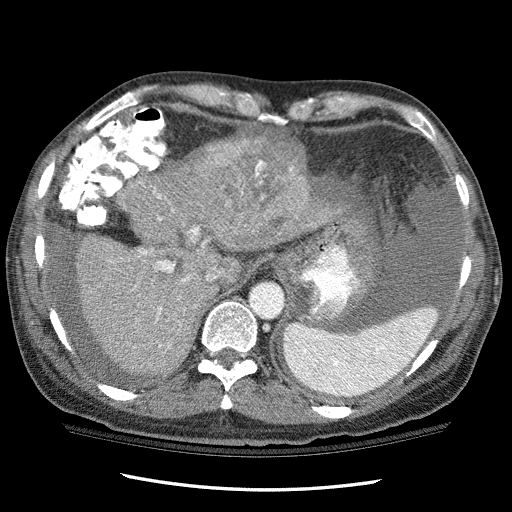
Contrast-enhanced abdominal CT (liver protocol), one axial slice; position 83 of 114 along the scan axis; 120 kVp; one of 3 acquisitions stored at this slice position; soft-tissue window (W 400 / L 40 HU); 2.5 mm slice thickness; 512 × 512 image matrix, field of view 360 × 360 mm. Case-level facts recorded for this patient, not image findings: diagnosis: hepatocellular carcinoma (patient treated with transarterial chemoembolisation; whether this scan precedes or follows treatment is not stated here); TNM stage (as recorded): Stage-I; Child-Pugh class: C; tumour nodularity: uninodular.
Structures marked on this image (semi-automatic segmentation, software-assisted and operator-edited):
- abdominal aorta: bounding box <250,284,284,318> (left, top, right, bottom; pixels)
- liver parenchyma outside the tumour (the mass and vessels are separate outlines, so this box may not span the whole liver): <76,158,330,374>
- mass: <192,128,311,244>
- liver vessels: <157,195,216,347>